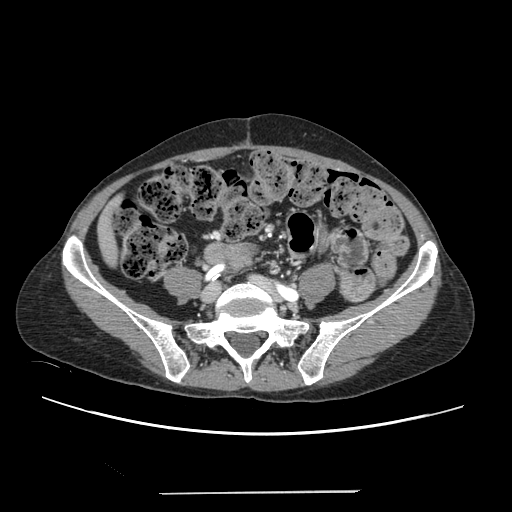
Contrast-enhanced abdominal CT, one axial slice. Slice 12 of 240 in the series (ordered by position). Intravenous contrast given. Soft-tissue window (W 400 / L 40 HU). 1.25 mm slice thickness. 512 × 512 image matrix. Female patient, age 60 years. Case-level facts recorded for this patient, not image findings: diagnosis: colorectal cancer liver metastases, imaged before liver resection; multiple liver metastases: no; largest metastasis: 1.5 cm; chemotherapy before resection: yes.
Annotated regions visible in this slice (outlined manually by an expert reader):
- liver: bounding box <100,213,116,262> (left, top, right, bottom; pixels)
- planned liver remnant (the part of the liver to remain after resection): <100,212,116,263>